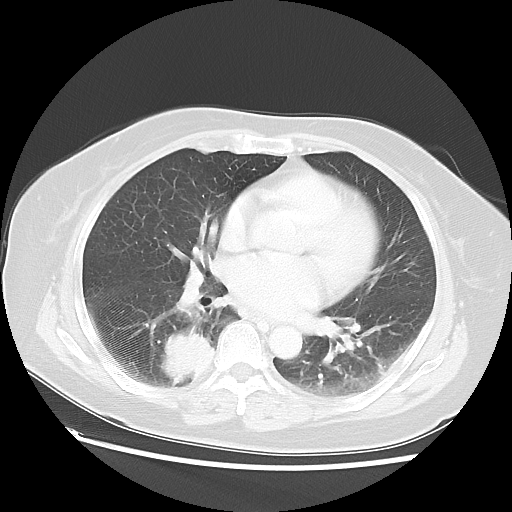
Chest CT, one axial slice. Position 27 of 52 along the scan axis. Lung window (W 1500 / L -600 HU). 512 × 512 image matrix. Female patient, age 69 years. Case-level facts recorded for this patient, not image findings: clinical TNM (as recorded): T2 N1 M1a.
Outlined on this slice (rectangle marked by the reading radiologist):
- lung tumour (recorded histology: adenocarcinoma): bounding box [x1, y1, x2, y2] px = [153, 318, 213, 389]